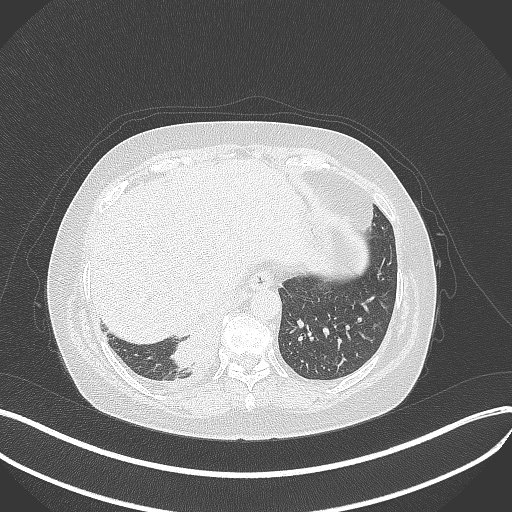
Chest CT, one axial slice. Slice 84 of 381 in the series (ordered by position). 120 kVp. Lung window (W 1500 / L -600 HU). 1 mm slice thickness. 512 × 512 image matrix, field of view 400 × 400 mm. Female patient, age 56 years. From the clinical record (not read from this slice): clinical TNM (as recorded): T2b N1 M0; histopathological grade: G3.
Structures marked on this image (bounding box drawn by a radiologist):
- lung tumour (recorded histology: small cell carcinoma): box from (x=171, y=325) to (x=223, y=373) px